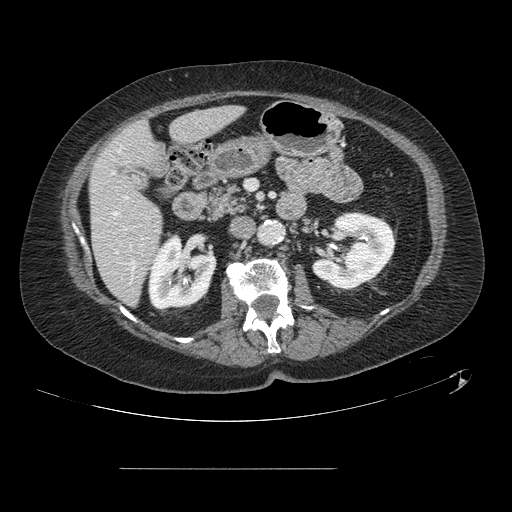
Contrast-enhanced abdominal CT, one axial slice. Position 48 of 148 along the scan axis. 120 kVp. Soft-tissue window (W 400 / L 40 HU). 512 × 512 image matrix. Female patient, age 75 years. Case-level facts recorded for this patient, not image findings: diagnosis: colorectal cancer liver metastases, imaged before liver resection; multiple liver metastases: no; largest metastasis: 2.4 cm; chemotherapy before resection: no.
Structures marked on this image (expert manual segmentation):
- hepatic veins: bounding box [x1, y1, x2, y2] px = [114, 212, 135, 269]
- liver: [90, 106, 240, 304]
- planned liver remnant (the part of the liver to remain after resection): [90, 106, 241, 304]